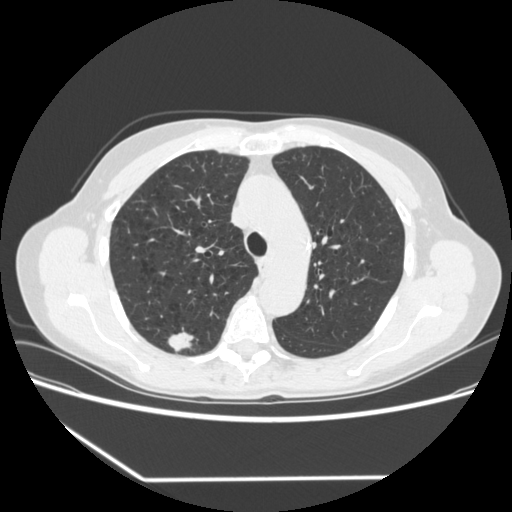
Axial slice from a low-dose chest CT screening exam; baseline annual screen; lung window (W 1500 / L -600 HU); 1.25 mm slice thickness; standard (soft-tissue) reconstruction kernel (STANDARD); slice 243 of 323 in the series. Female participant, aged 67 years at enrolment. Current smoker at enrolment.
- Expert-annotated lung lesion, bounding box <156,323,200,359> (left, top, right, bottom; pixels).
- The screening reader recorded 2 non-calcified nodules or masses ≥4 mm on this exam (right upper lobe, right lower lobe); which of them this box marks is not recorded.
- Participant outcome: lung cancer diagnosed 29 days after this screen — adenocarcinoma, NOS, right upper lobe, moderately differentiated (G2), stage IA (AJCC 6th edition), 24 mm at pathology.